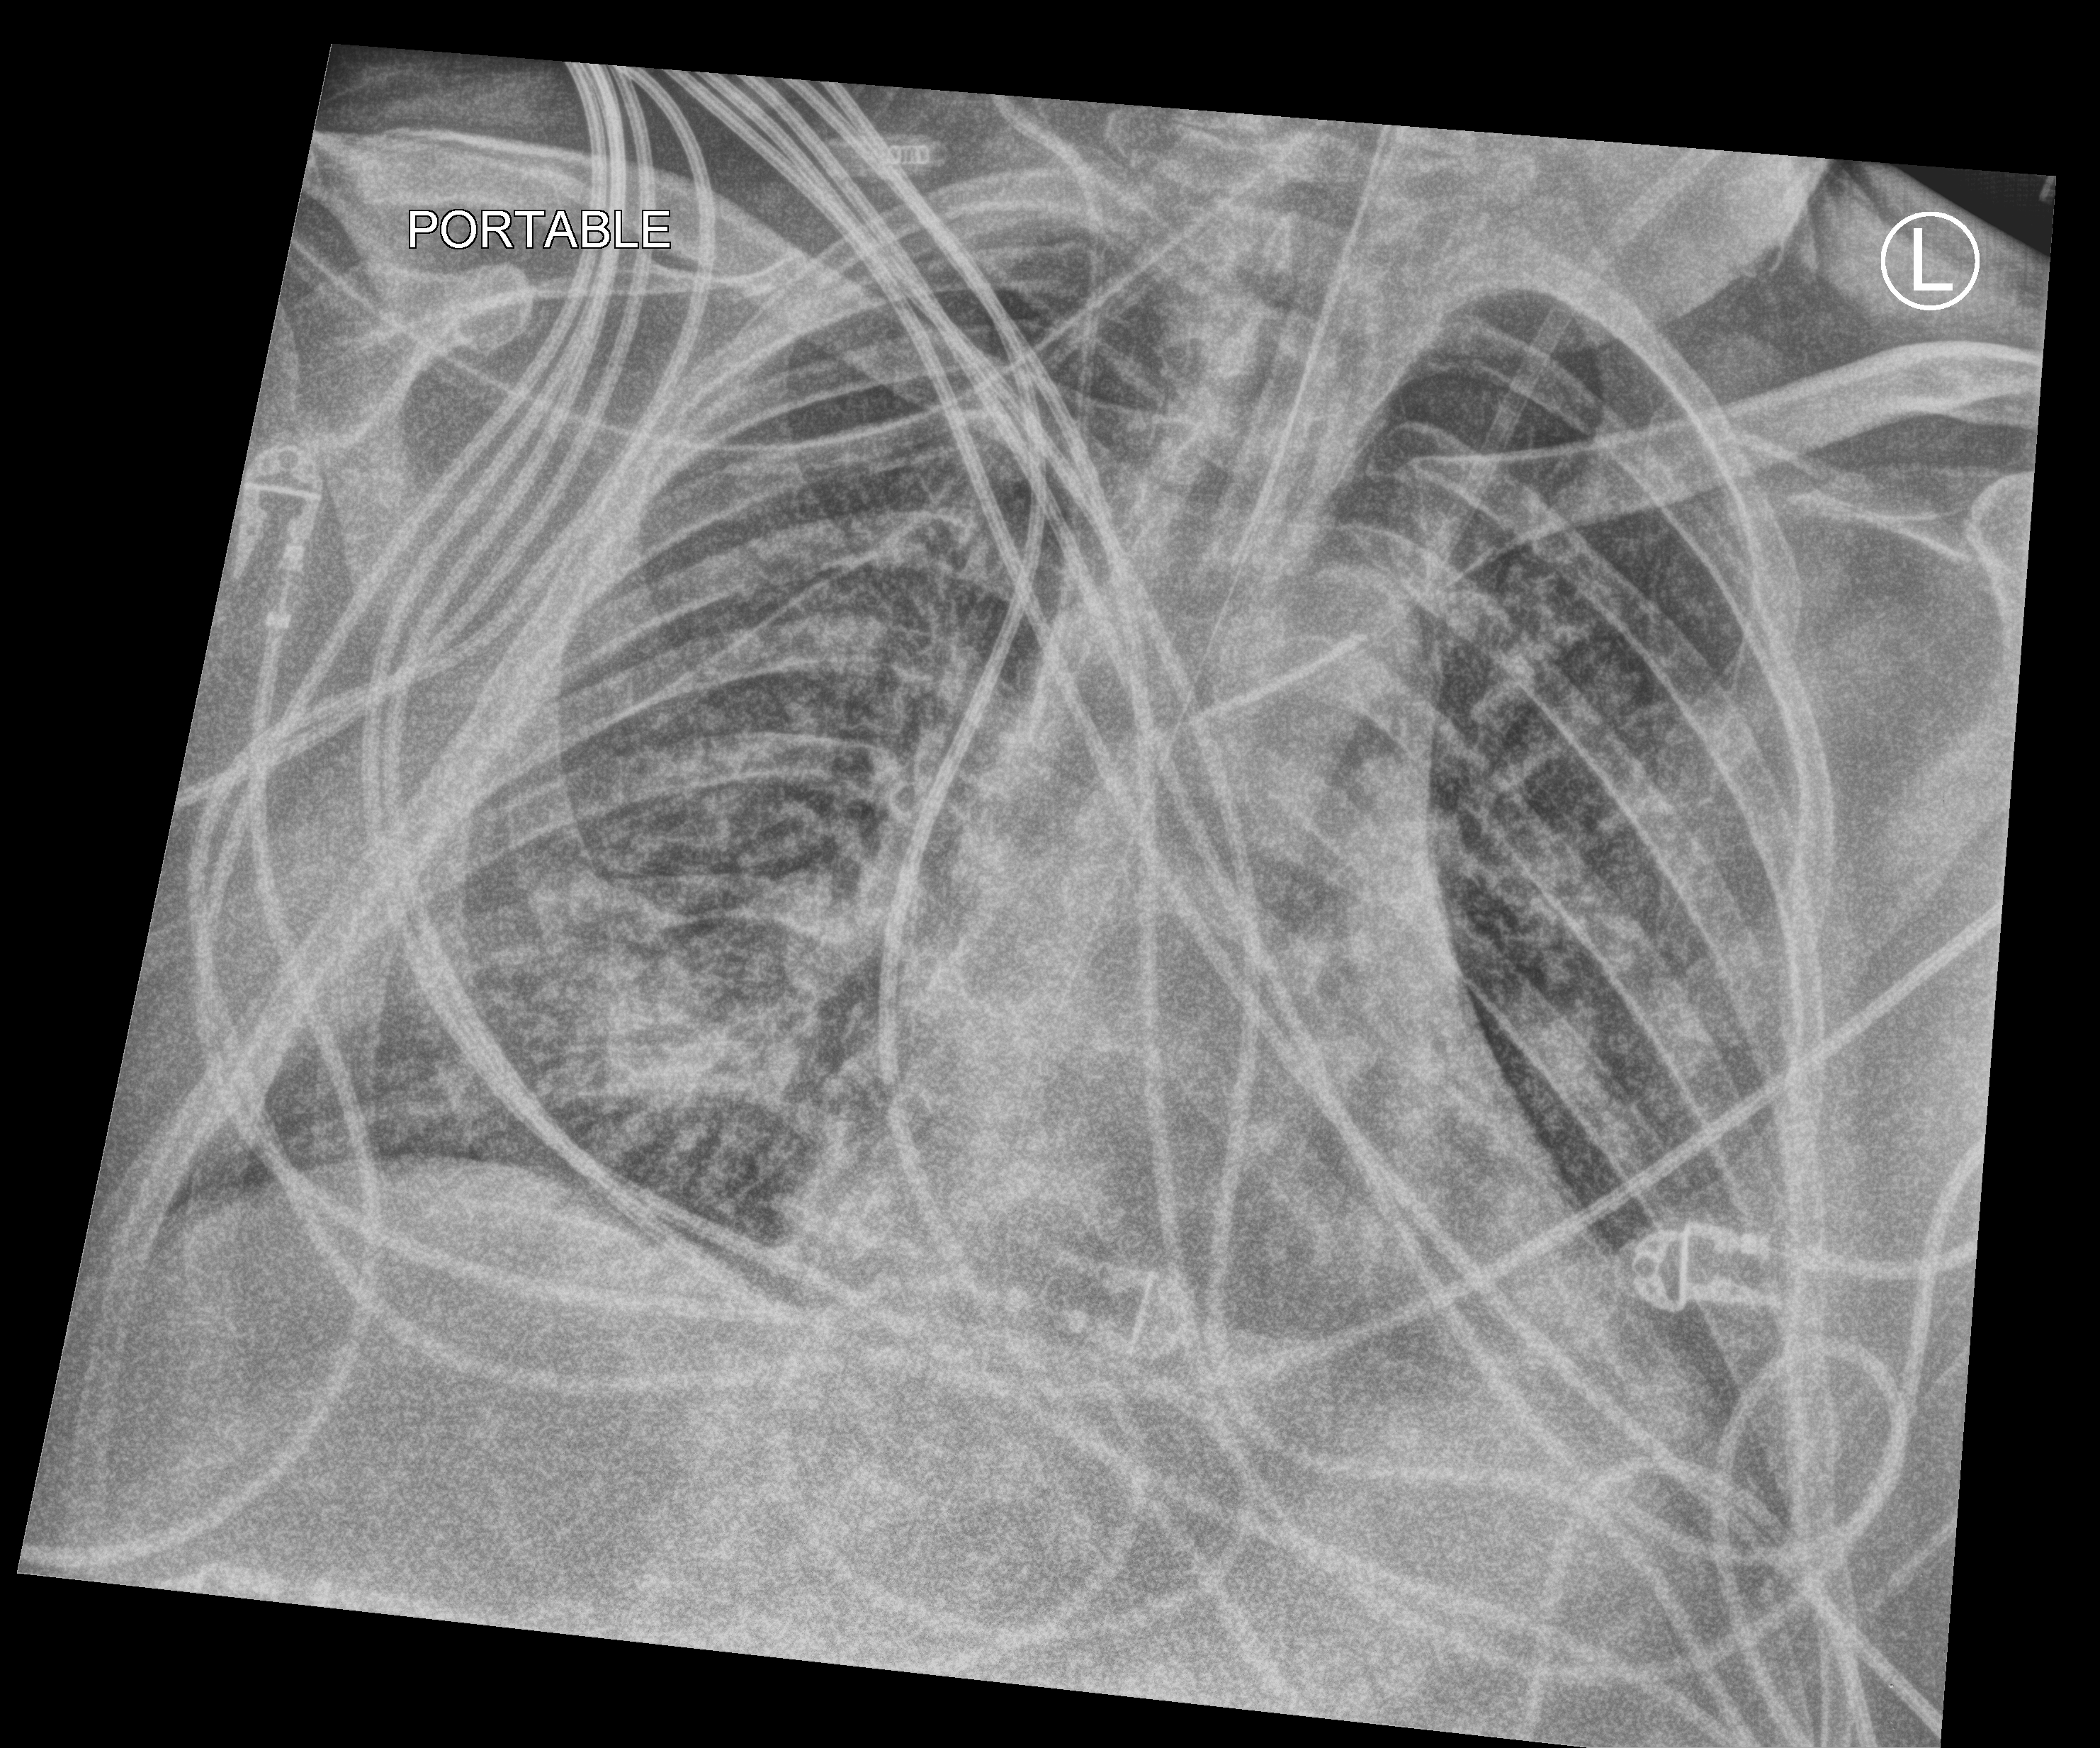
Chest X-ray (portable); anteroposterior (AP) projection. Patient hospitalised with COVID-19; male, aged 18–59 years.
From the hospital-stay record, not from the radiograph (when in the stay this image was taken is not recorded): admitted to intensive care during this hospital stay: yes; mechanically ventilated during this hospital stay: yes; diabetes (admission record): no.